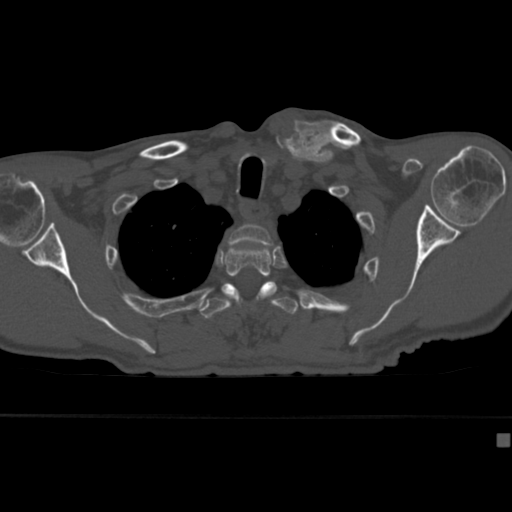
CT including the spine, one axial slice; position 330 of 430 along the scan axis; reconstruction kernel Br40s; bone window (W 1800 / L 400 HU); 1.5 mm slice thickness; 512 × 512 image matrix, field of view 337 × 337 mm. Male patient, age 64 years. From the clinical record (not read from this slice): primary cancer: uterus.
Structures marked on this image (semi-automatically segmented with operator editing):
- T2 vertebra: box from (x=228, y=224) to (x=273, y=248) px
- T3 vertebra: (x=223, y=245)–(x=277, y=287)
- T4 vertebra: (x=201, y=283)–(x=298, y=319)